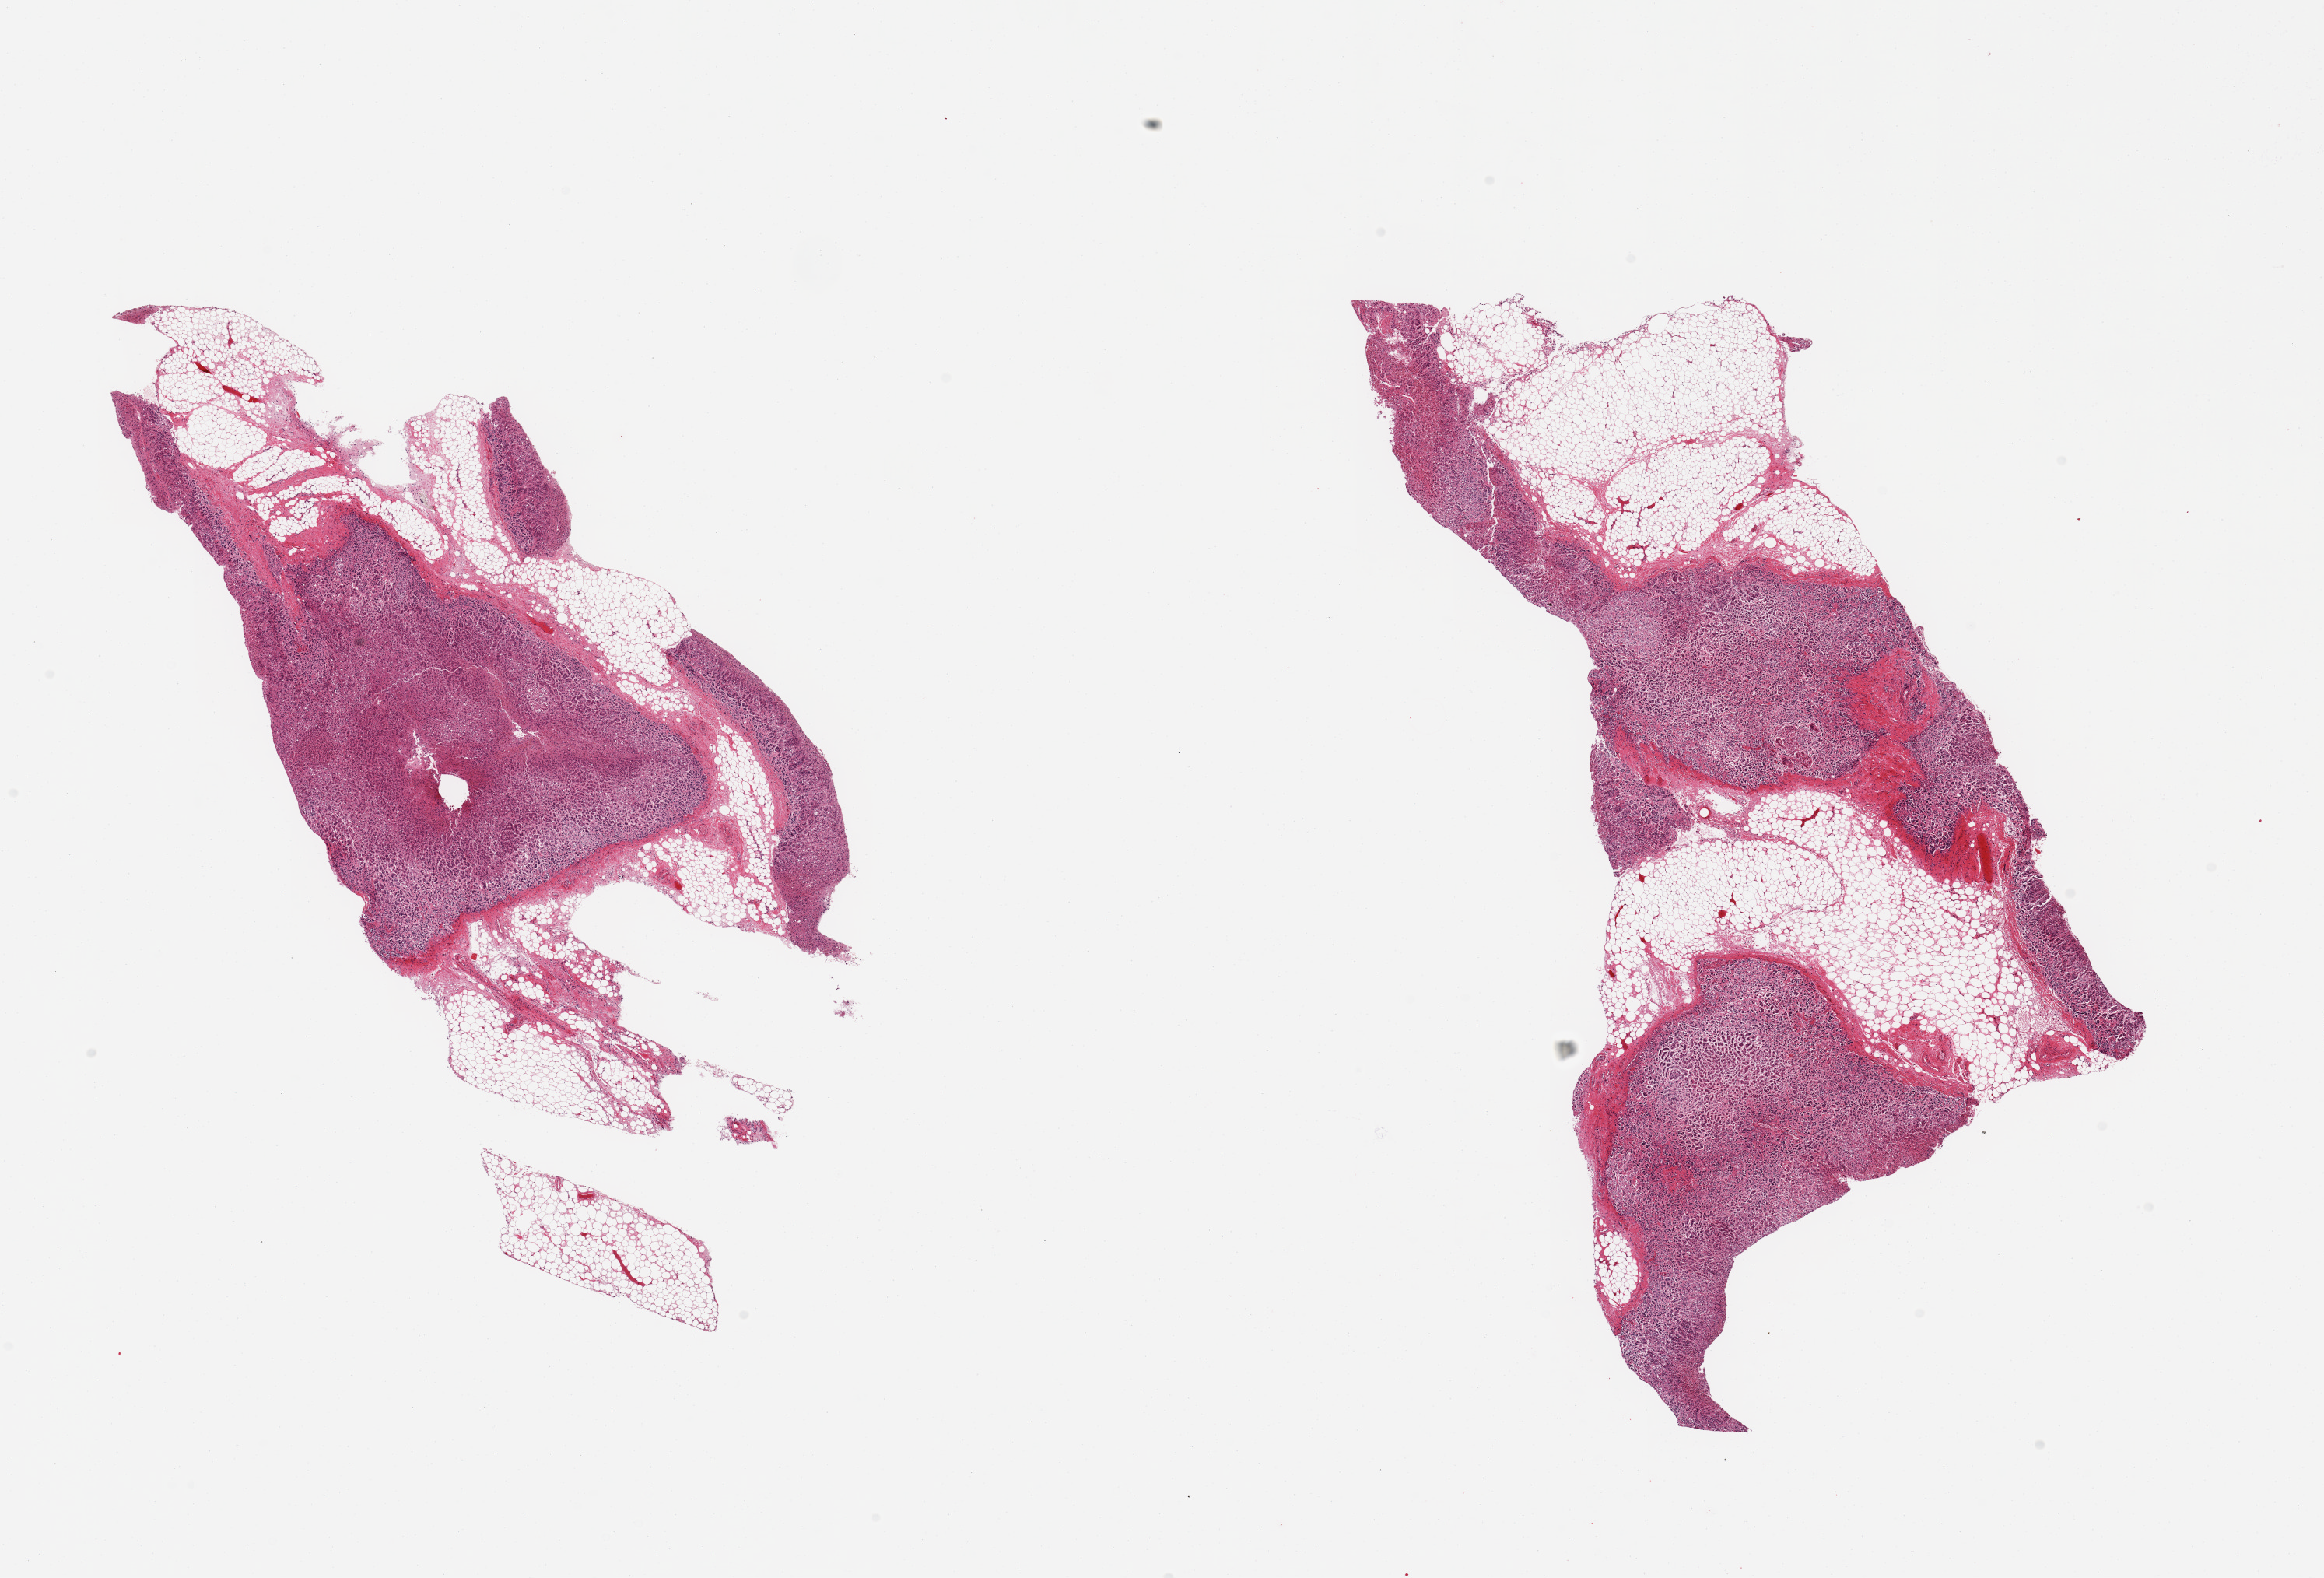
Digitized hematoxylin and eosin (H&E)-stained section, shown as a low-resolution overview of the whole scanned area (about 23.6 x 16.0 mm, acquisition: 20x scan). PAXgene-fixed, paraffin-embedded tissue. Target tissue: adrenal gland. Tissue donor sample. Donor sex: female.
Review note (as recorded): 2 pieces; 30-40% of each is fat.